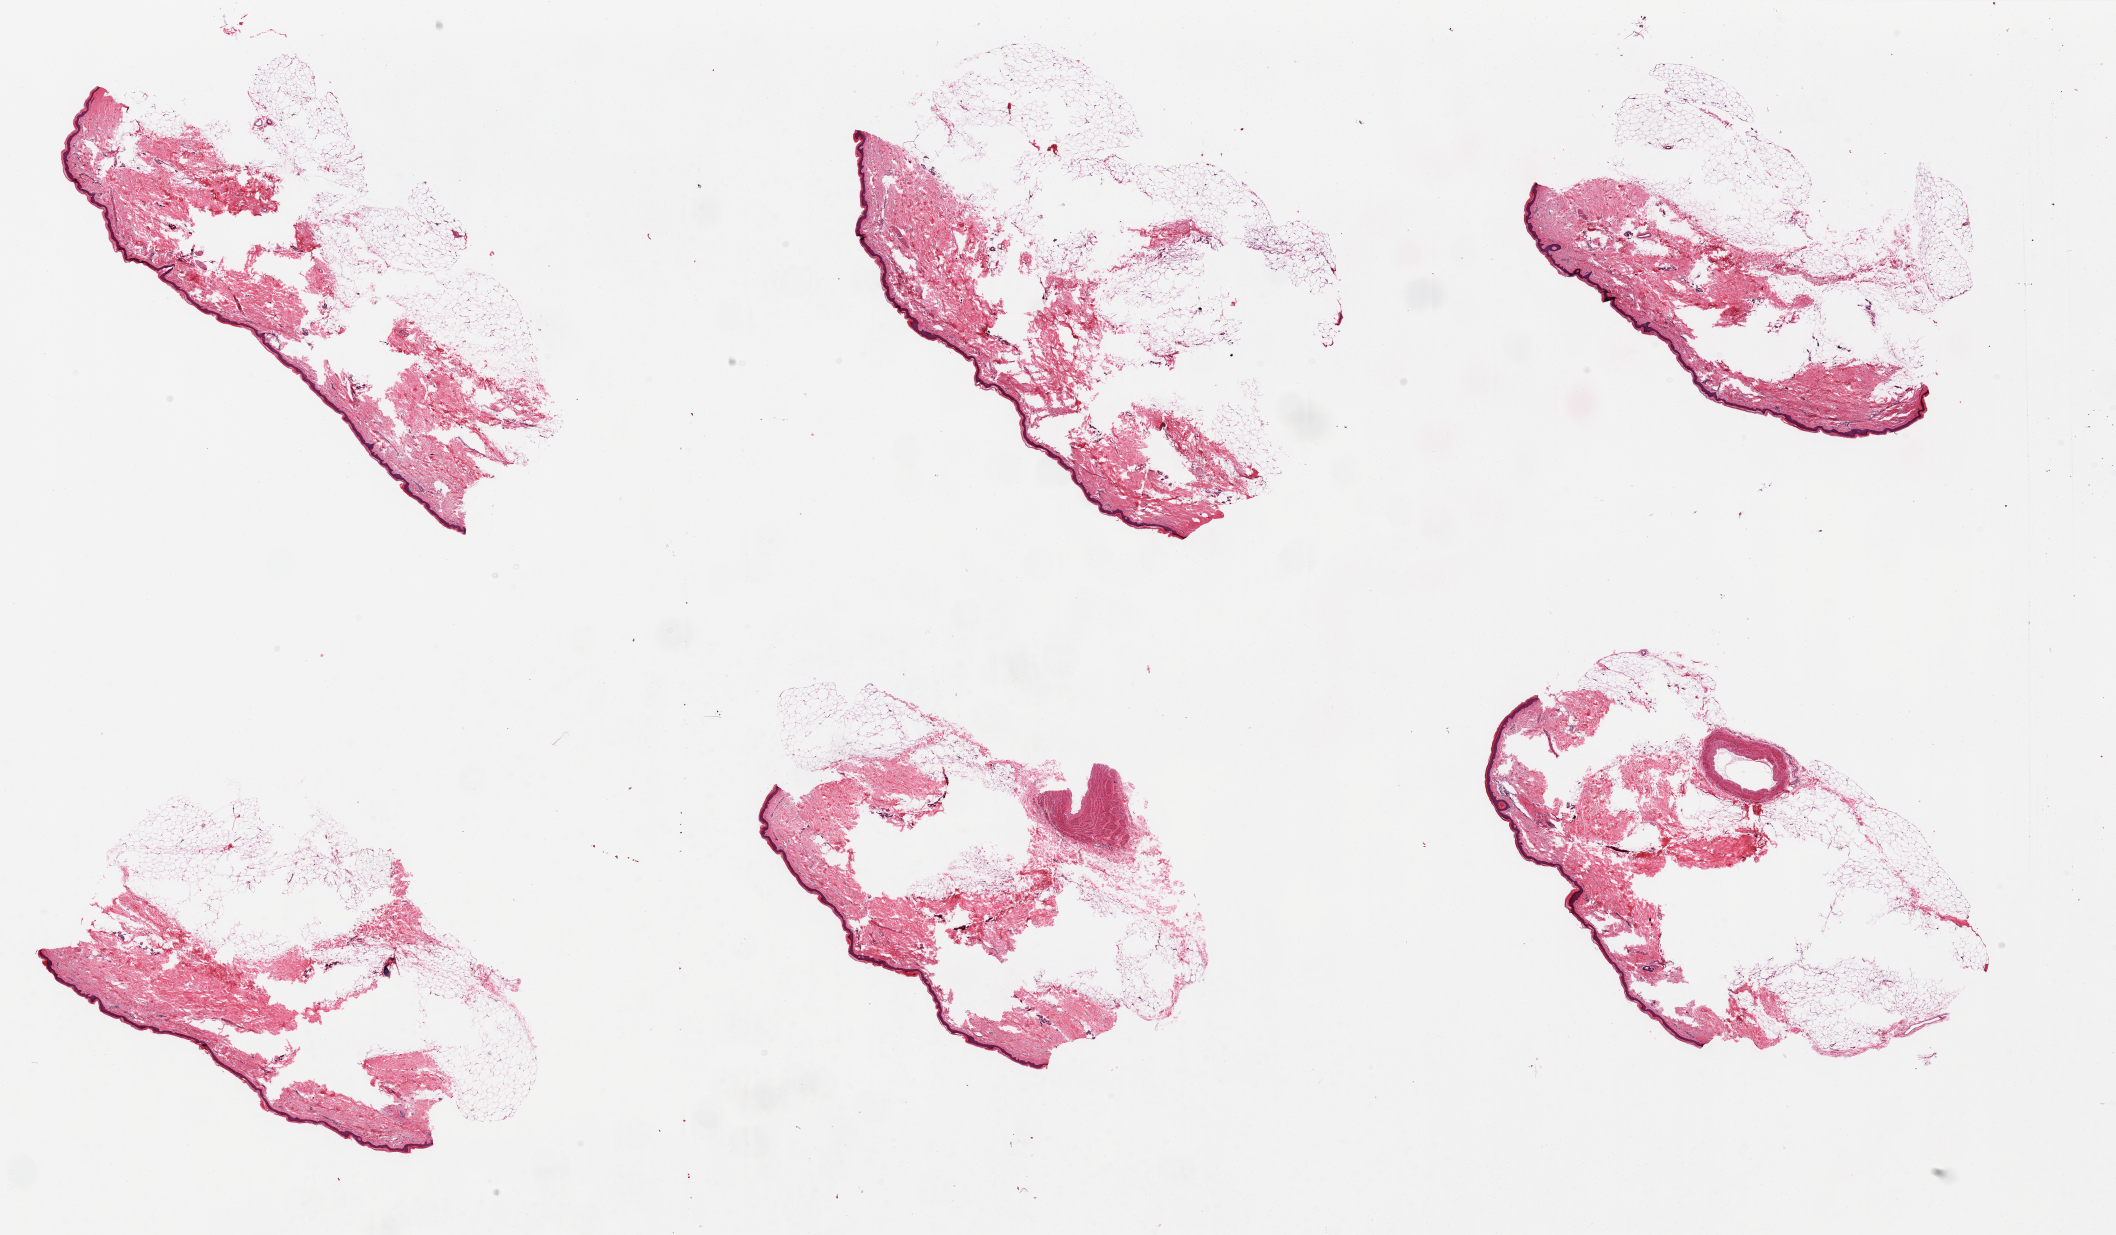
Digitized hematoxylin and eosin (H&E)-stained section, brightfield — low-resolution overview of the scanned area, about 33.5 x 19.5 mm (from a 20x scan); PAXgene-fixed, paraffin-embedded tissue; sampled site (target tissue): skin of lower leg; tissue donor sample. Donor: female.
Pathologist's review note for this sample: 6 pieces, all with significant attached adipose tissue, likely 50+%, central holes (? poor fixation), squamous epithelium is 27 to 44 microns thick.